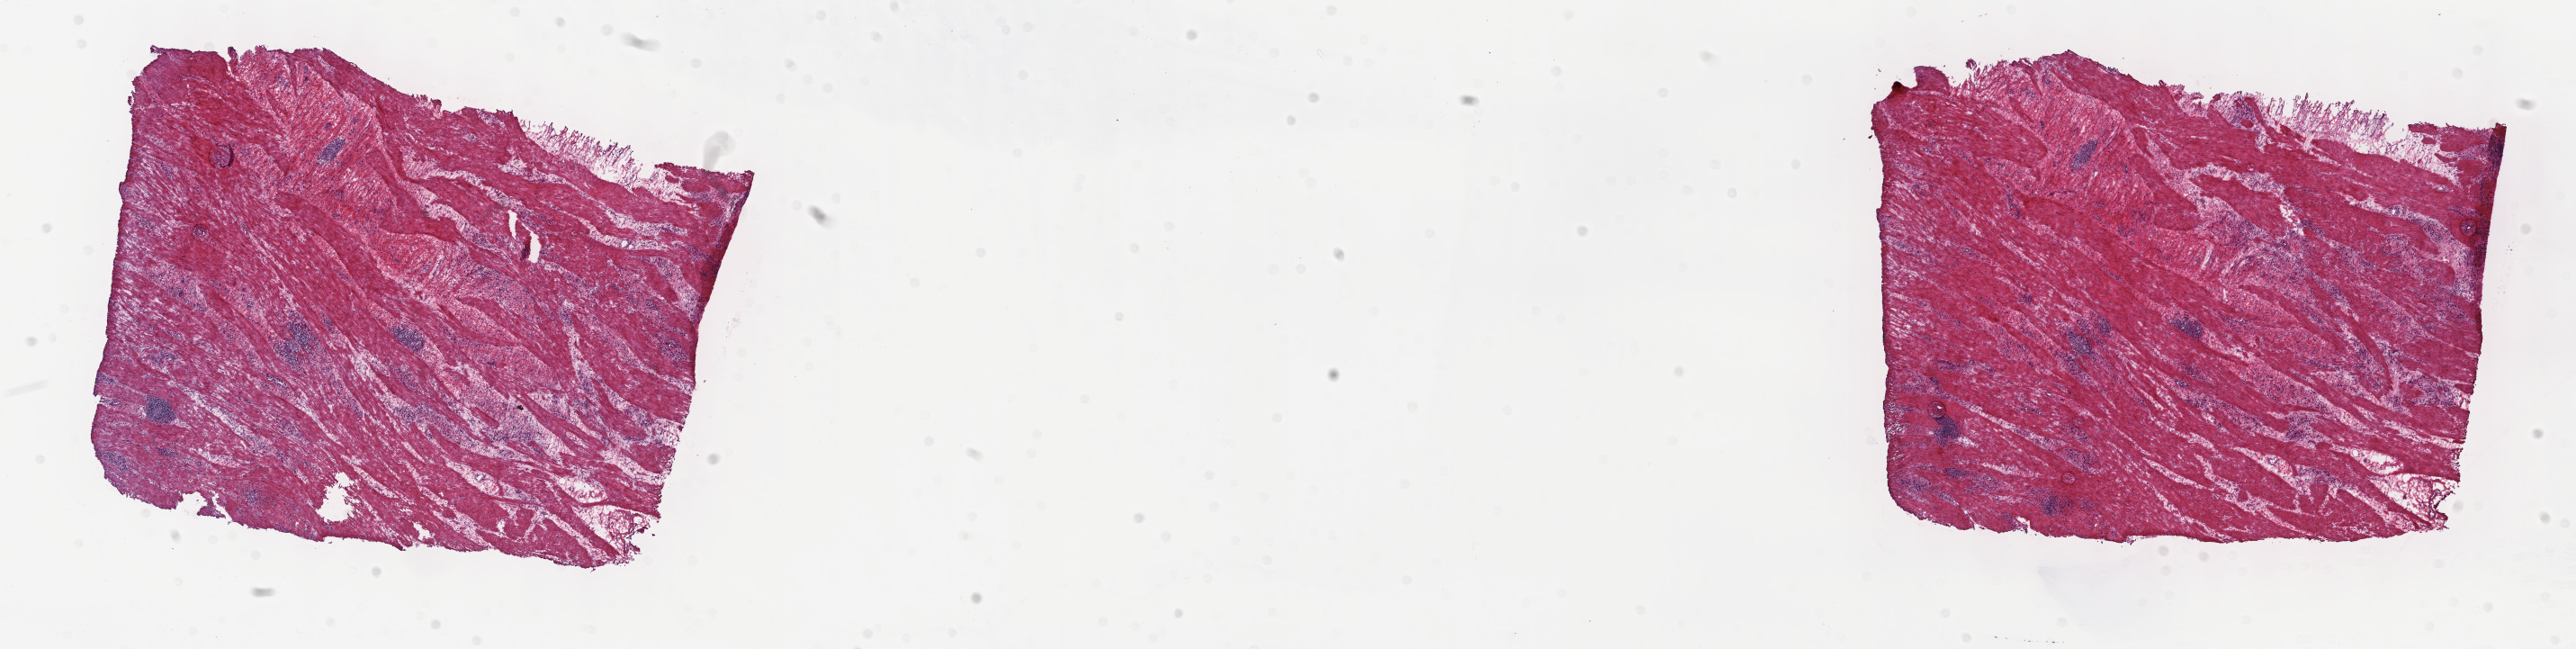
Hematoxylin and eosin (H&E) stained whole-slide image — whole scanned area (about 23.2 x 5.8 mm, from a 40x scan) shown as a low-resolution overview. Frozen section from the top of the tissue portion. Sample: primary tumour, stomach. Patient: female, age at initial diagnosis 59 years. Composition of this section per pathologist review: tumour cells 100%, tumour nuclei 10%.
Histologic diagnosis: Carcinoma, diffuse type (gastric antrum).